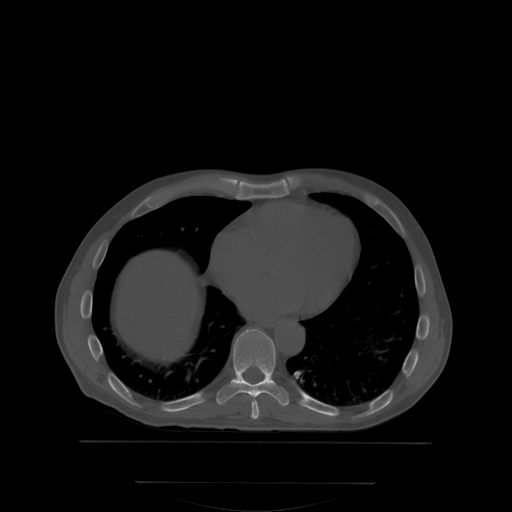
CT including the spine, one axial slice; position 205 of 350 along the scan axis; bone window (W 1800 / L 400 HU); 2.5 mm slice thickness; 512 × 512 image matrix, field of view 500 × 500 mm. Patient: male, 58 years. Case-level facts recorded for this patient, not image findings: primary cancer: prostate; vertebrae with lytic lesions (as recorded): L1.
Outlined on this slice (semi-automatically segmented with operator editing):
- T8 vertebra: bounding box (x1, y1, x2, y2) in pixels: (251, 400, 260, 418)
- T9 vertebra: (217, 328, 289, 405)